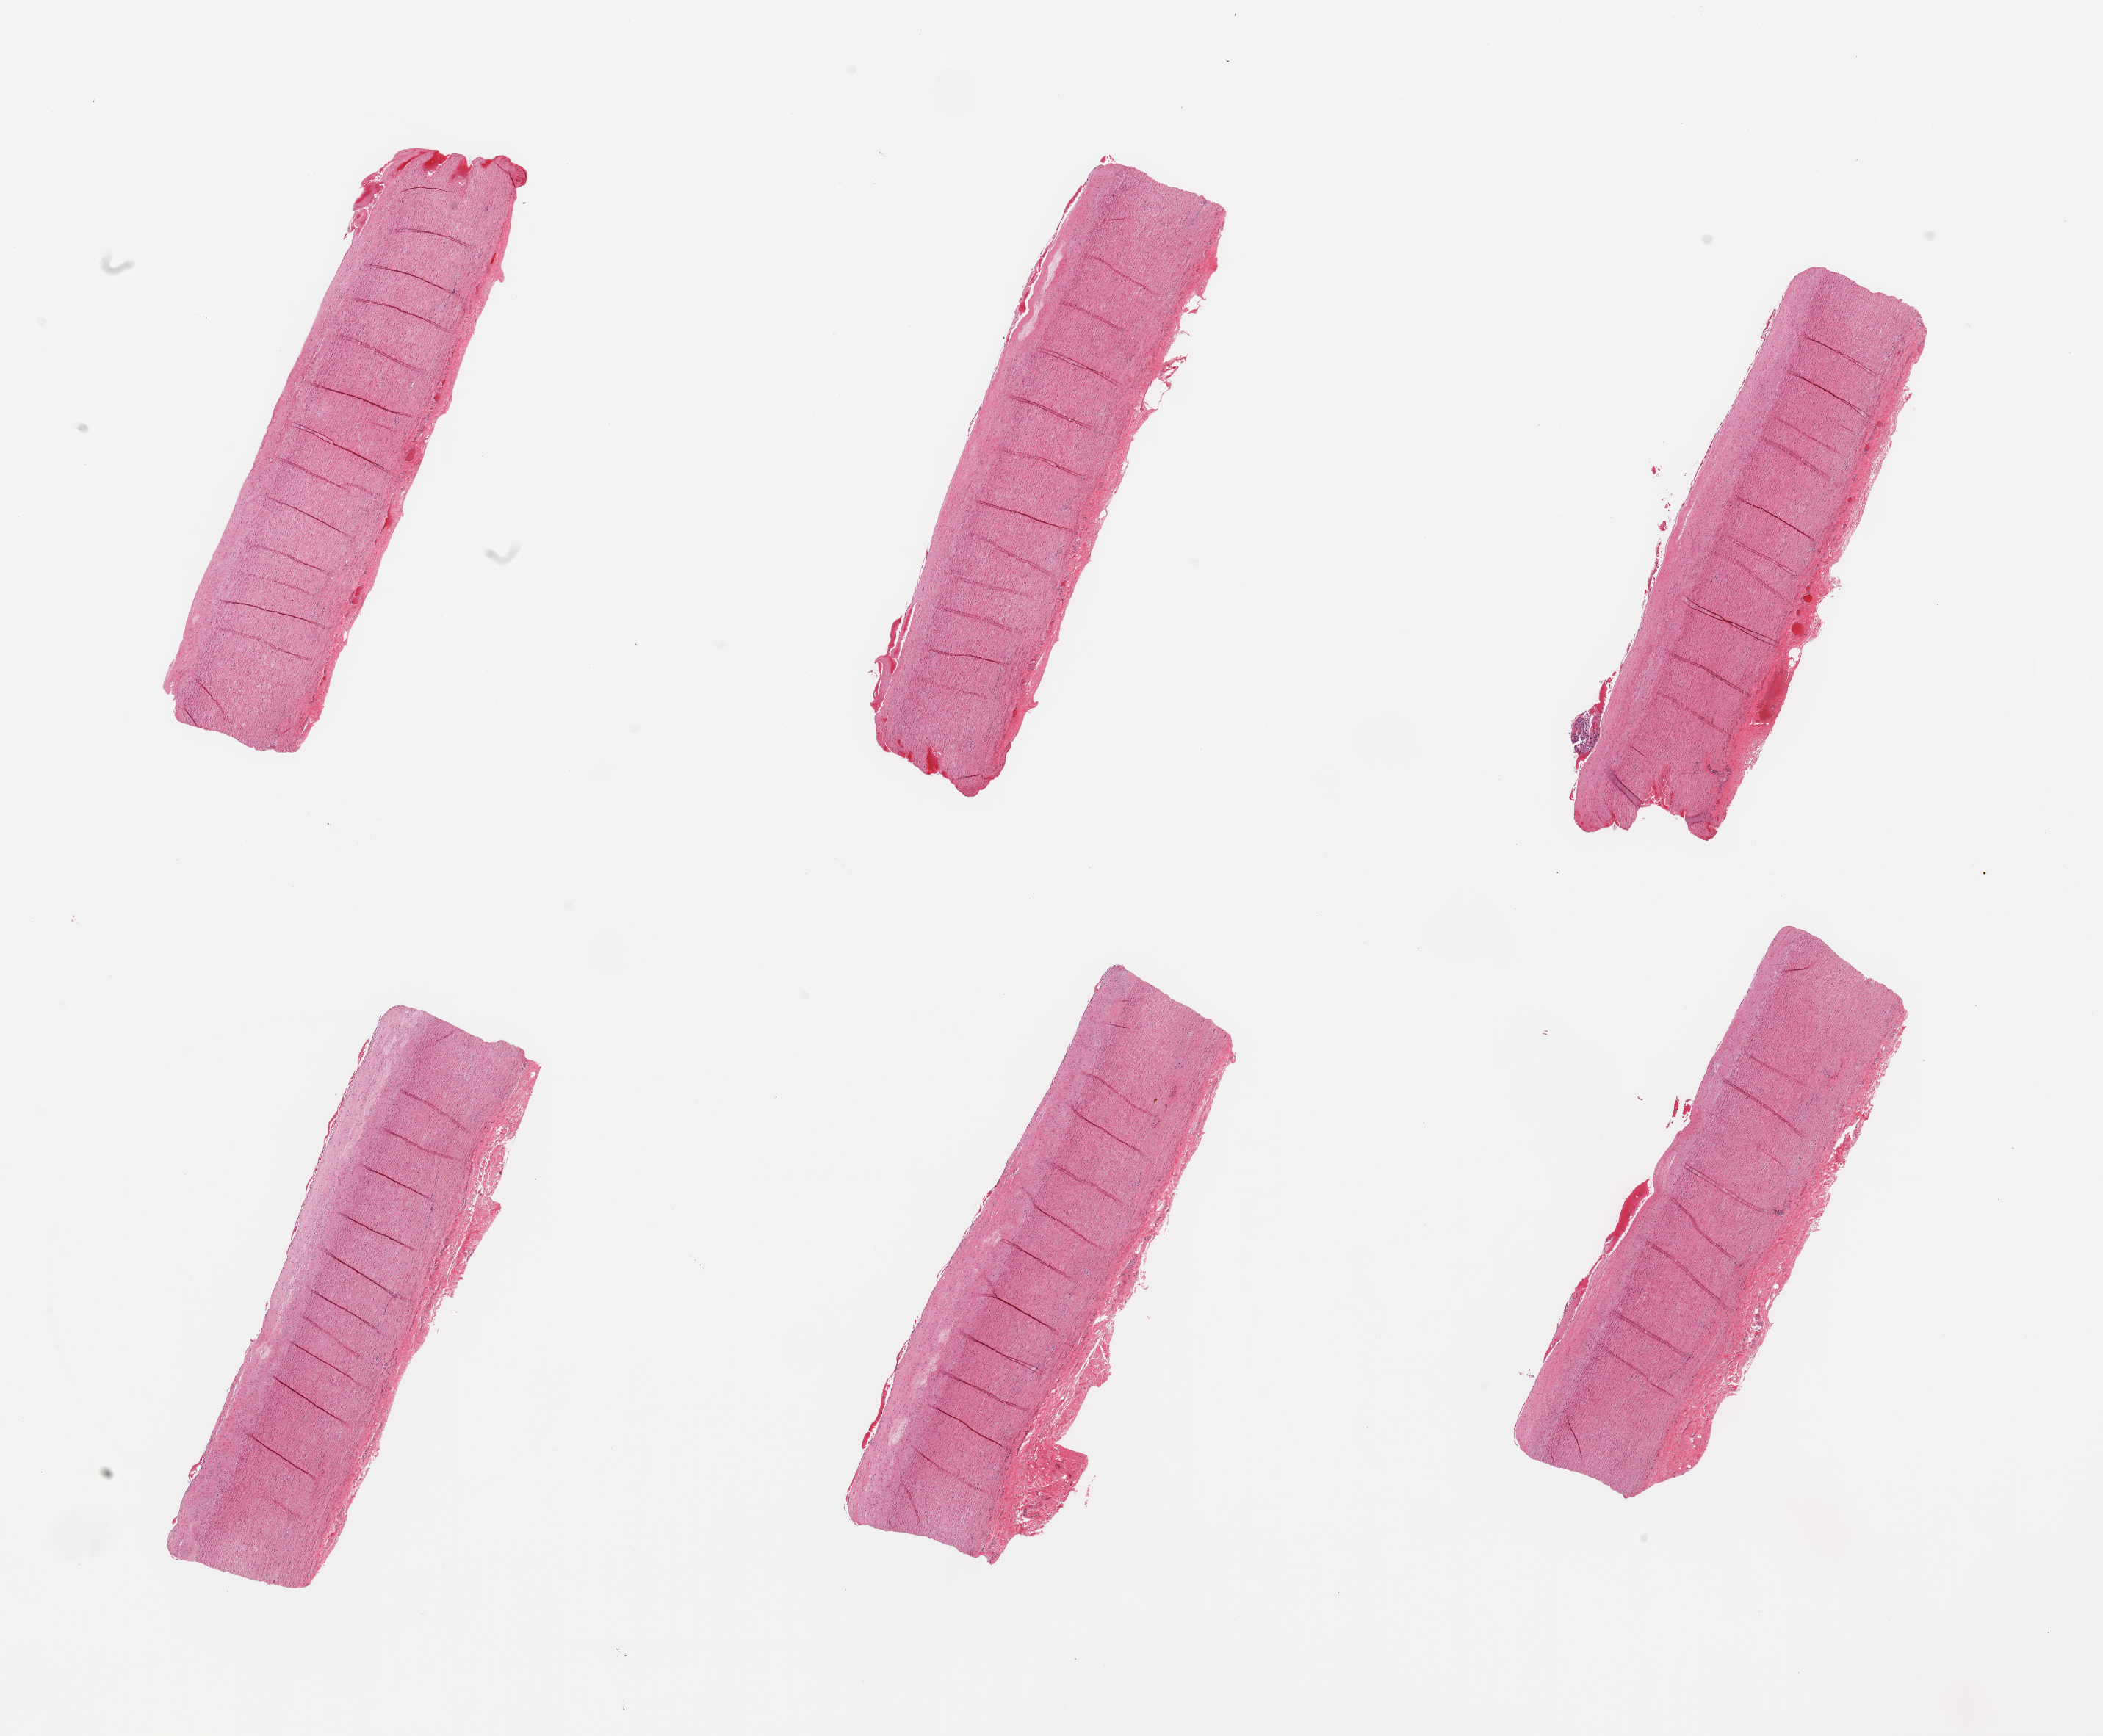
Digitized haematoxylin and eosin-stained section — low-resolution overview of the scanned area, about 22.6 x 18.7 mm; PAXgene-fixed paraffin-embedded (PFPE) section; section of aorta (target tissue); donor tissue sample. Male donor.
* pathologist's review note for this sample: 6 pieces, atherosis up to ~0.3-0.4mm